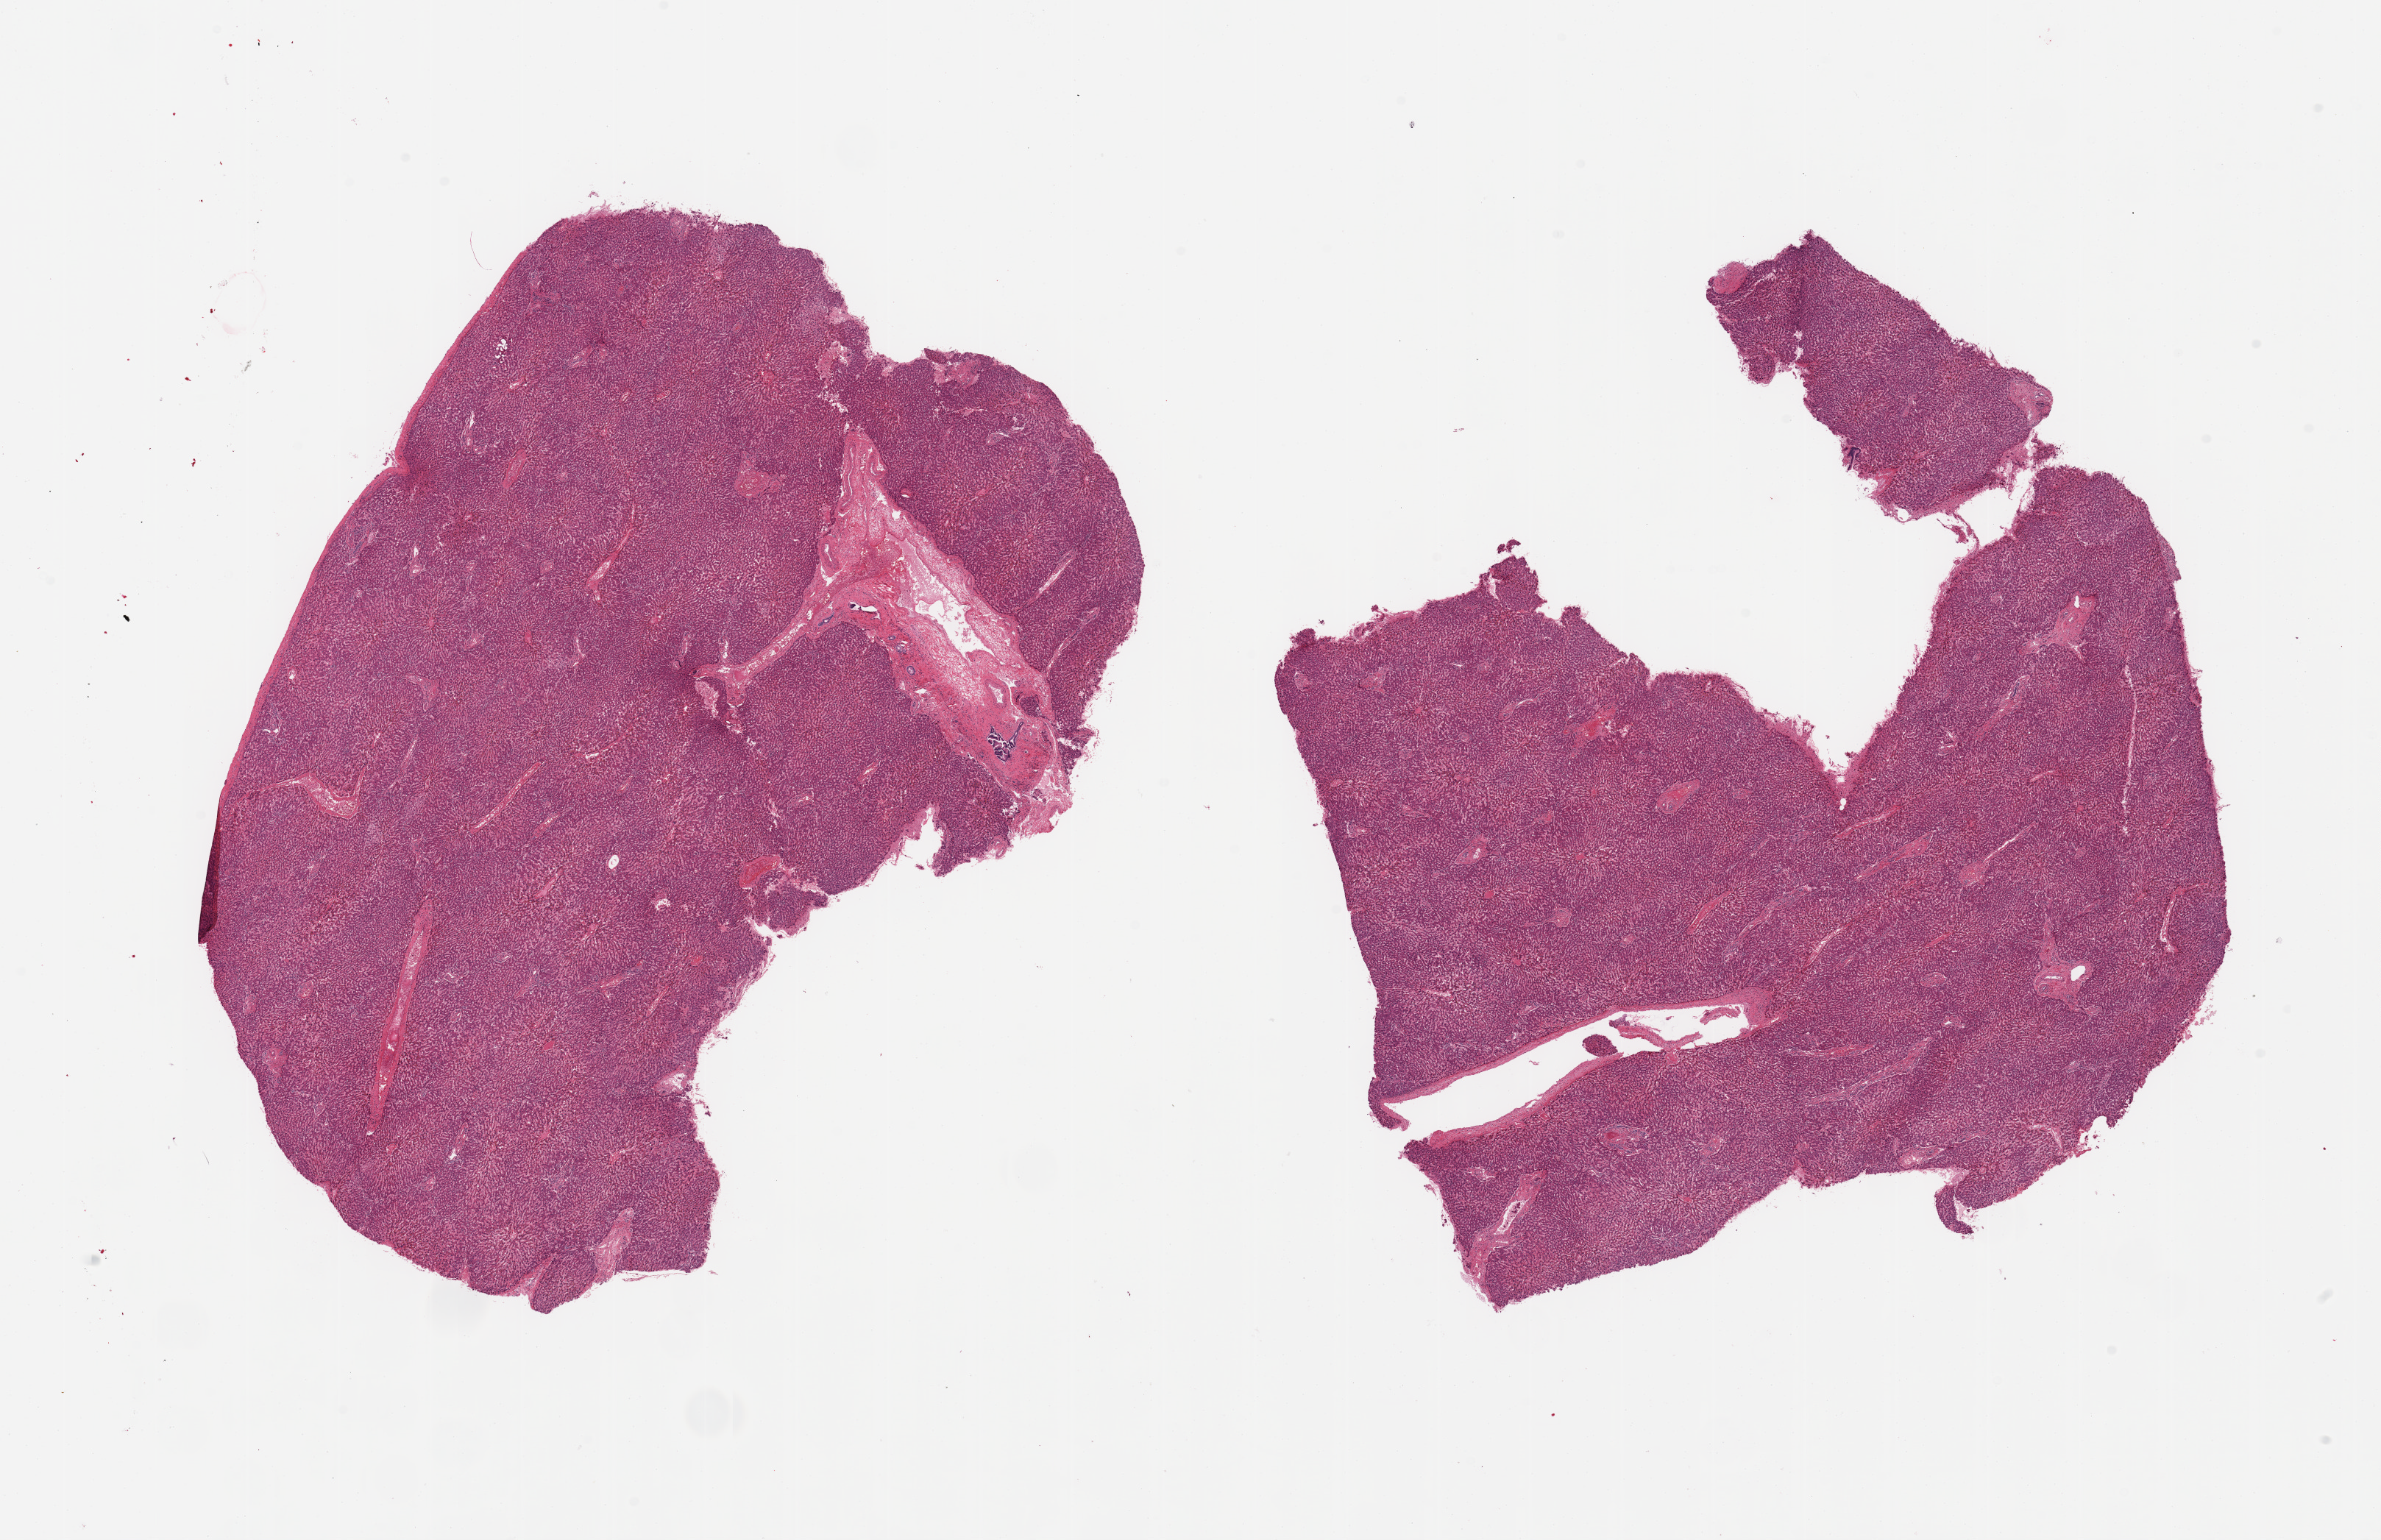
Whole-slide image, hematoxylin and eosin (H&E) stain — low-resolution overview of the scanned area, about 25.6 x 16.6 mm, PAXgene-fixed paraffin-embedded (PFPE) section, section of liver (target tissue), tissue donor sample. Female donor.
Reviewer comment on this tissue sample: 2 pieces, minimal congestion.